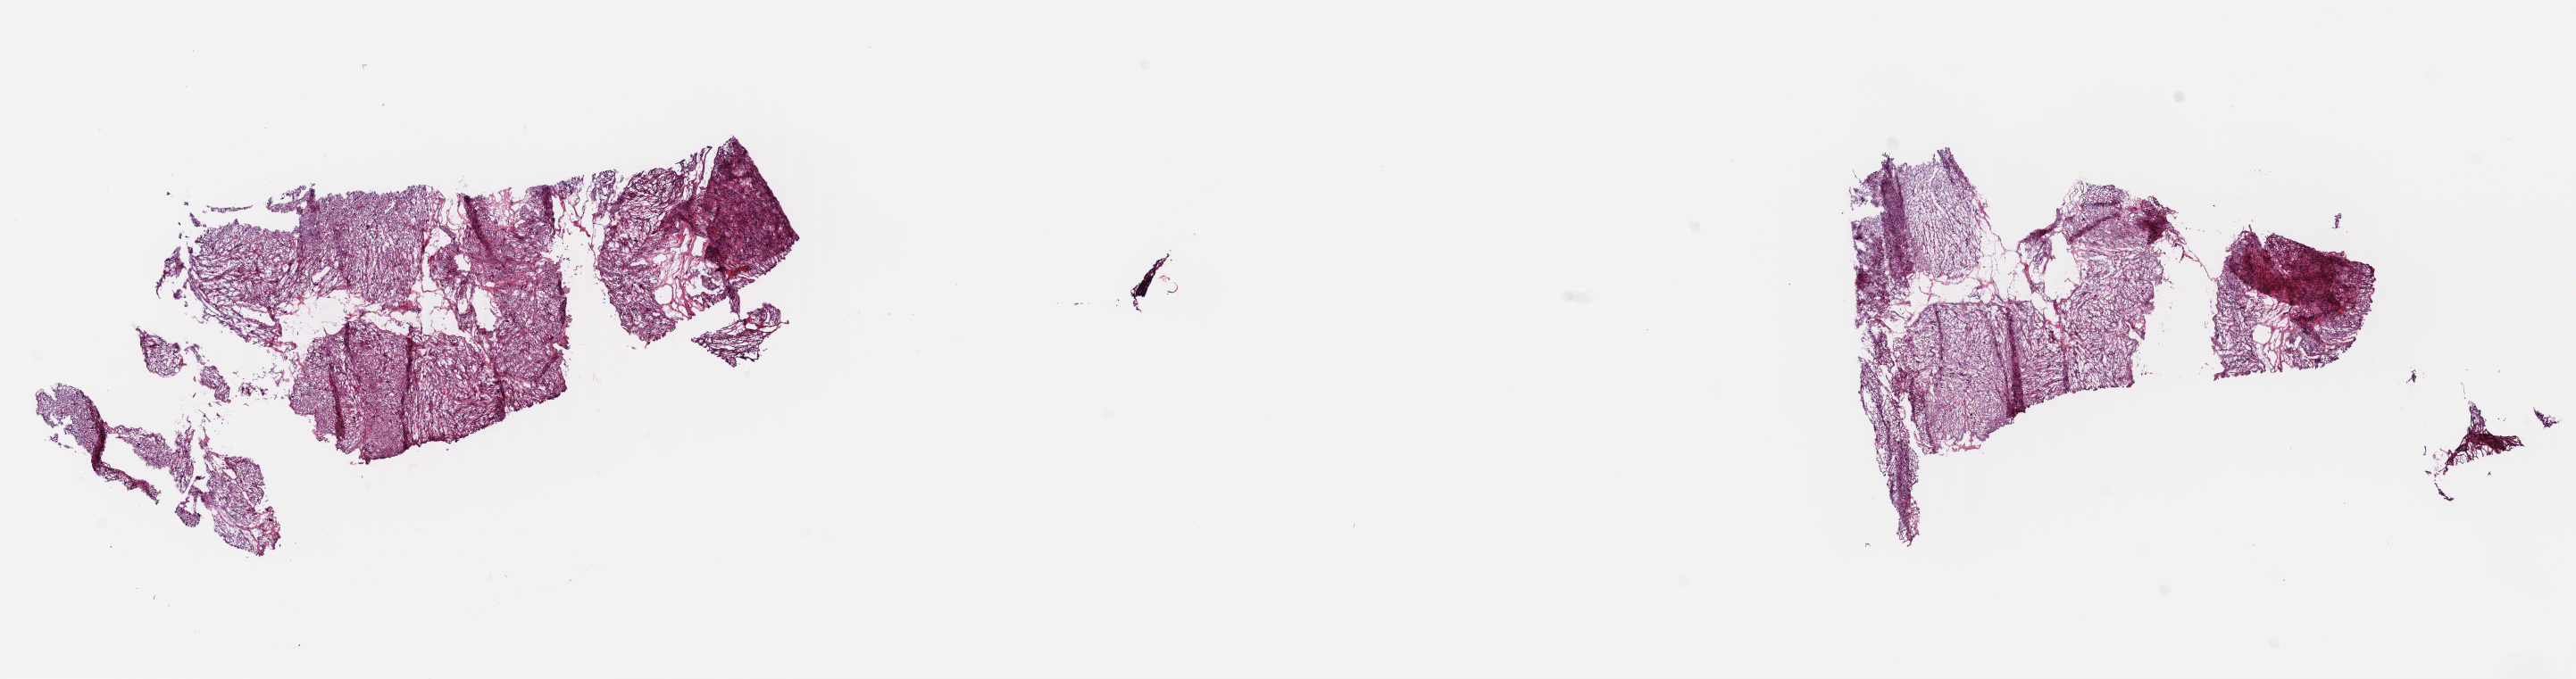
Whole-slide histology image, H&E-stained, whole scanned area (about 22.7 x 6.0 mm) shown as a low-resolution overview. Frozen section from the top of the tissue portion. Retroperitoneum and peritoneum, primary tumour sample. Female patient. Pathologist review of this section (percent, as recorded): tumour cells 75%, tumour nuclei 75%, normal cells 0%, stromal cells 25%, necrosis 0%. Inflammatory infiltration, as recorded: lymphocyte infiltration 2%, monocyte infiltration 2%, neutrophil infiltration 1%.
• pathologic diagnosis: Leiomyosarcoma, NOS (retroperitoneum)